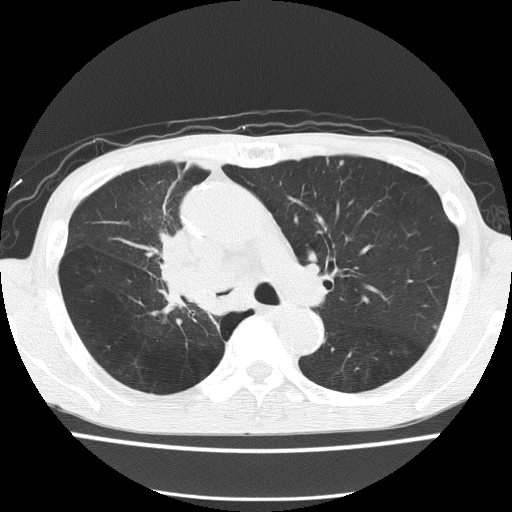
Axial slice from a low-dose chest CT screening exam. First (baseline) screen. Lung window (W 1500 / L -600 HU). Slice 55 of 150 in the series. 512 × 512 image matrix. Male participant, aged 59 years at enrolment.
Expert-annotated lung lesion, box from (x=141, y=230) to (x=233, y=321) px. The screening reader recorded 5 non-calcified nodules or masses ≥4 mm on this exam (left upper lobe, left upper lobe, left upper lobe, right middle lobe, right lower lobe); which of them this box marks is not recorded. Official screen result: positive, change unspecified: nodule(s) >= 4 mm or enlarging nodule(s), mass(es), or other non-specific abnormalities suspicious for lung cancer. Lung cancer was diagnosed 72 days after this screen: squamous cell carcinoma, NOS, right upper lobe, moderately differentiated (G2), stage IV (AJCC 6th edition).